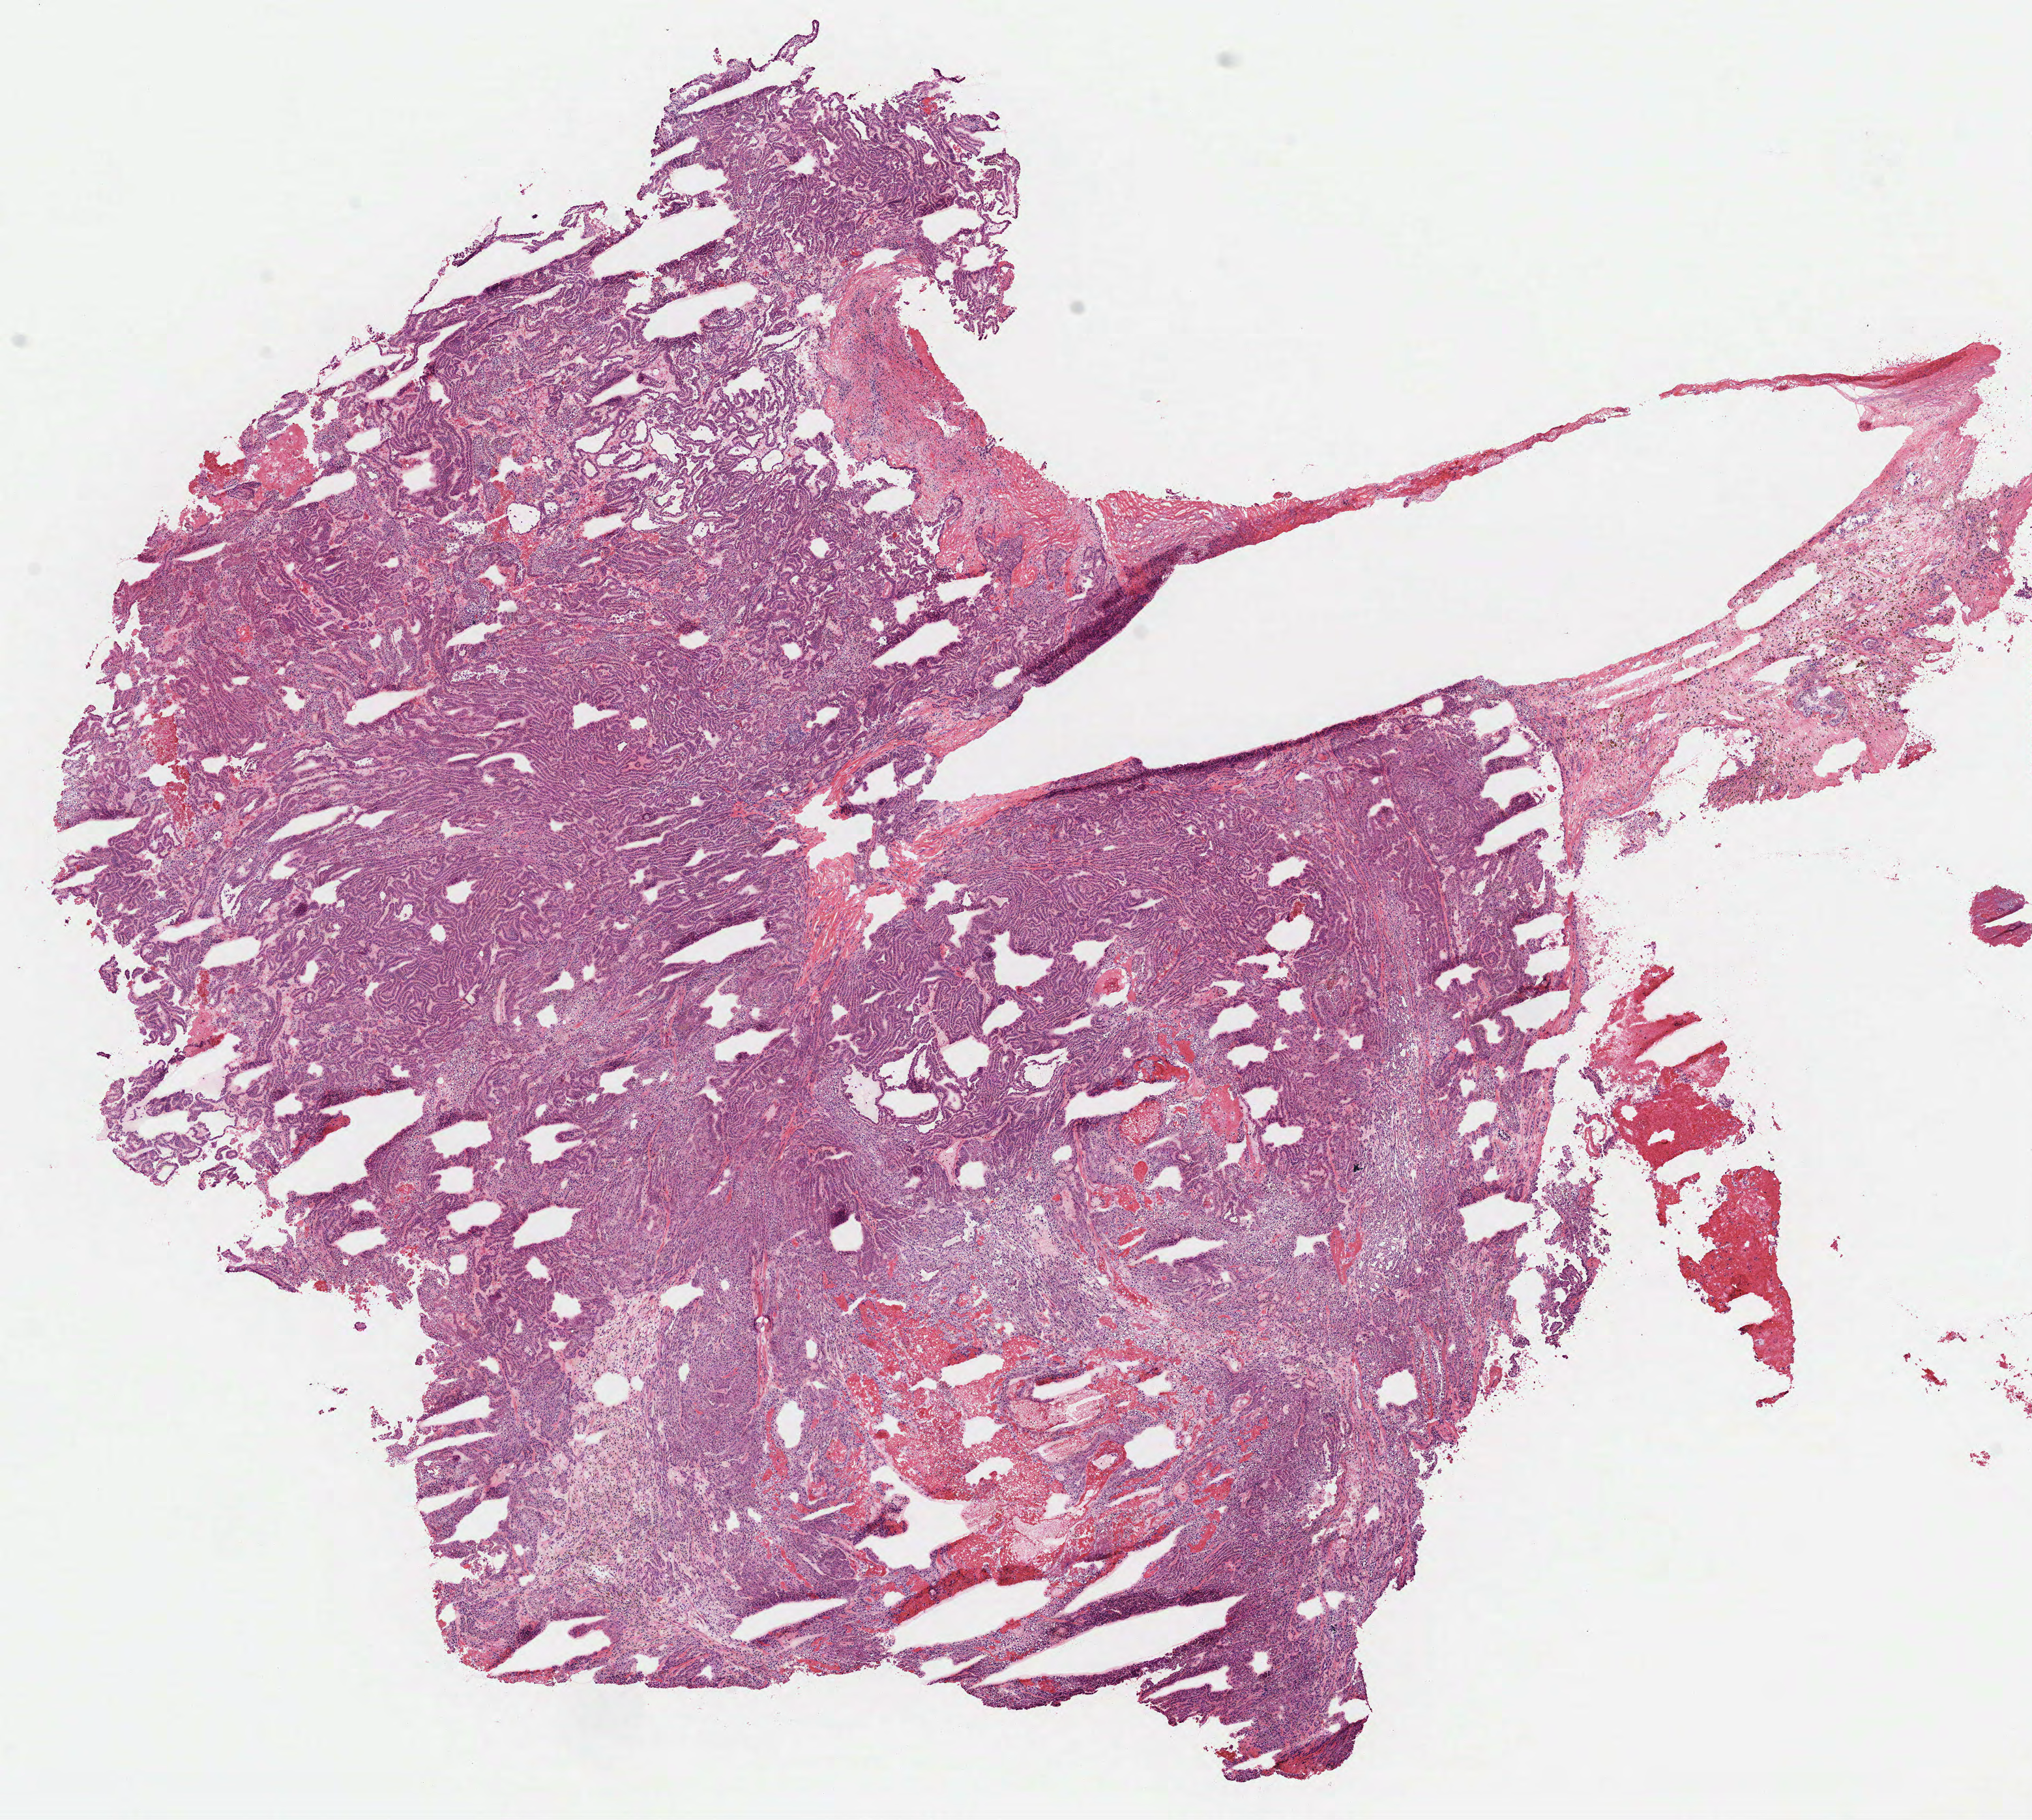
Whole-slide histology image, Hematoxylin and eosin (H&E) stained — low-resolution overview of the scanned area, about 12.6 x 11.3 mm. Frozen section. Primary tumour sample from the kidney. Male patient; age at initial diagnosis 73 years. Pathologist review of this section (percent, as recorded): tumour cells 100%, tumour nuclei 90%, normal cells 0%, stromal cells 0%, necrosis 0%. Inflammatory infiltration, as recorded: lymphocyte infiltration 3%, monocyte infiltration 1%, neutrophil infiltration 1%.
Laterality: left. AJCC pathologic stage: III (5th edition). Pathologic diagnosis: Papillary adenocarcinoma, NOS.